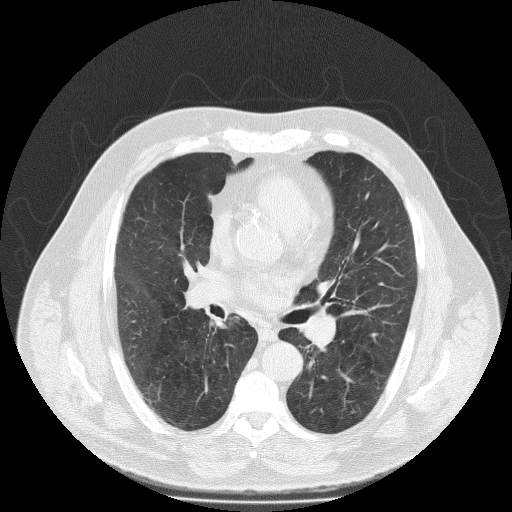
Chest CT (low-dose screening protocol), one axial image. Baseline screening round. Lung window (W 1500 / L -600 HU). 512 × 512 image matrix. Male, age 65 years at enrolment.
Expert reader's lesion annotation, bounding box <217,307,247,335> (left, top, right, bottom; pixels). The screening reader recorded 2 non-calcified nodules or masses ≥4 mm on this exam (right lower lobe, right middle lobe); which of them this box marks is not recorded. Official screen result: positive, change unspecified: nodule(s) >= 4 mm or enlarging nodule(s), mass(es), or other non-specific abnormalities suspicious for lung cancer.